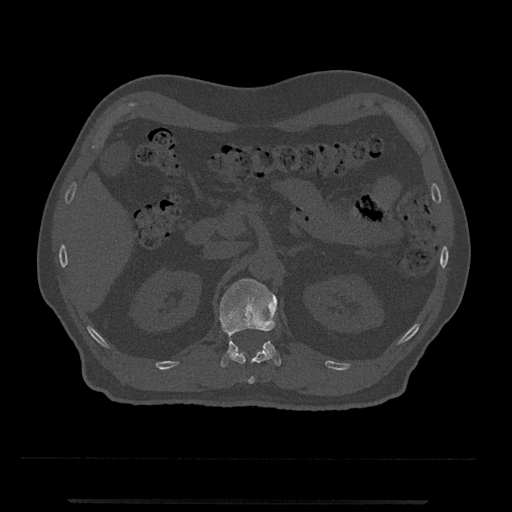
CT including the spine, one axial slice. Position 365 of 797 along the scan axis. 120 kVp. Bone window (W 1800 / L 400 HU). 0.5 mm slice thickness. 512 × 512 image matrix, field of view 419 × 419 mm. Patient: male, 63 years. Case-level facts recorded for this patient, not image findings: primary cancer: prostate.
Outlined on this slice (semi-automatically segmented with operator editing):
- L1 vertebra: box from (x=219, y=278) to (x=281, y=368) px
- T12 vertebra: (x=231, y=348)–(x=270, y=384)